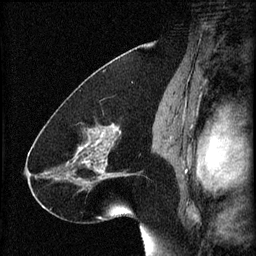
Breast MRI (dynamic contrast-enhanced), one sagittal slice; position 37 of 60 along the scan axis; 3 images stored at this slice position (order not interpretable as contrast timing); 1.5 T; TE 4.2 ms, TR 8.2 ms; 2 mm slice thickness; 256 × 256 image matrix, field of view 180 × 180 mm. Patient: female, 41 years.
Outlined on this slice (semi-automatically segmented with operator editing):
- analysis volume of interest (the breast-tissue region the enhancement analysis was run in; not a lesion): bounding box [x1, y1, x2, y2] px = [72, 126, 134, 193]
- tumour enhancement mask (voxels above the 70 % enhancement threshold inside the analysis volume of interest): [74, 126, 129, 183]